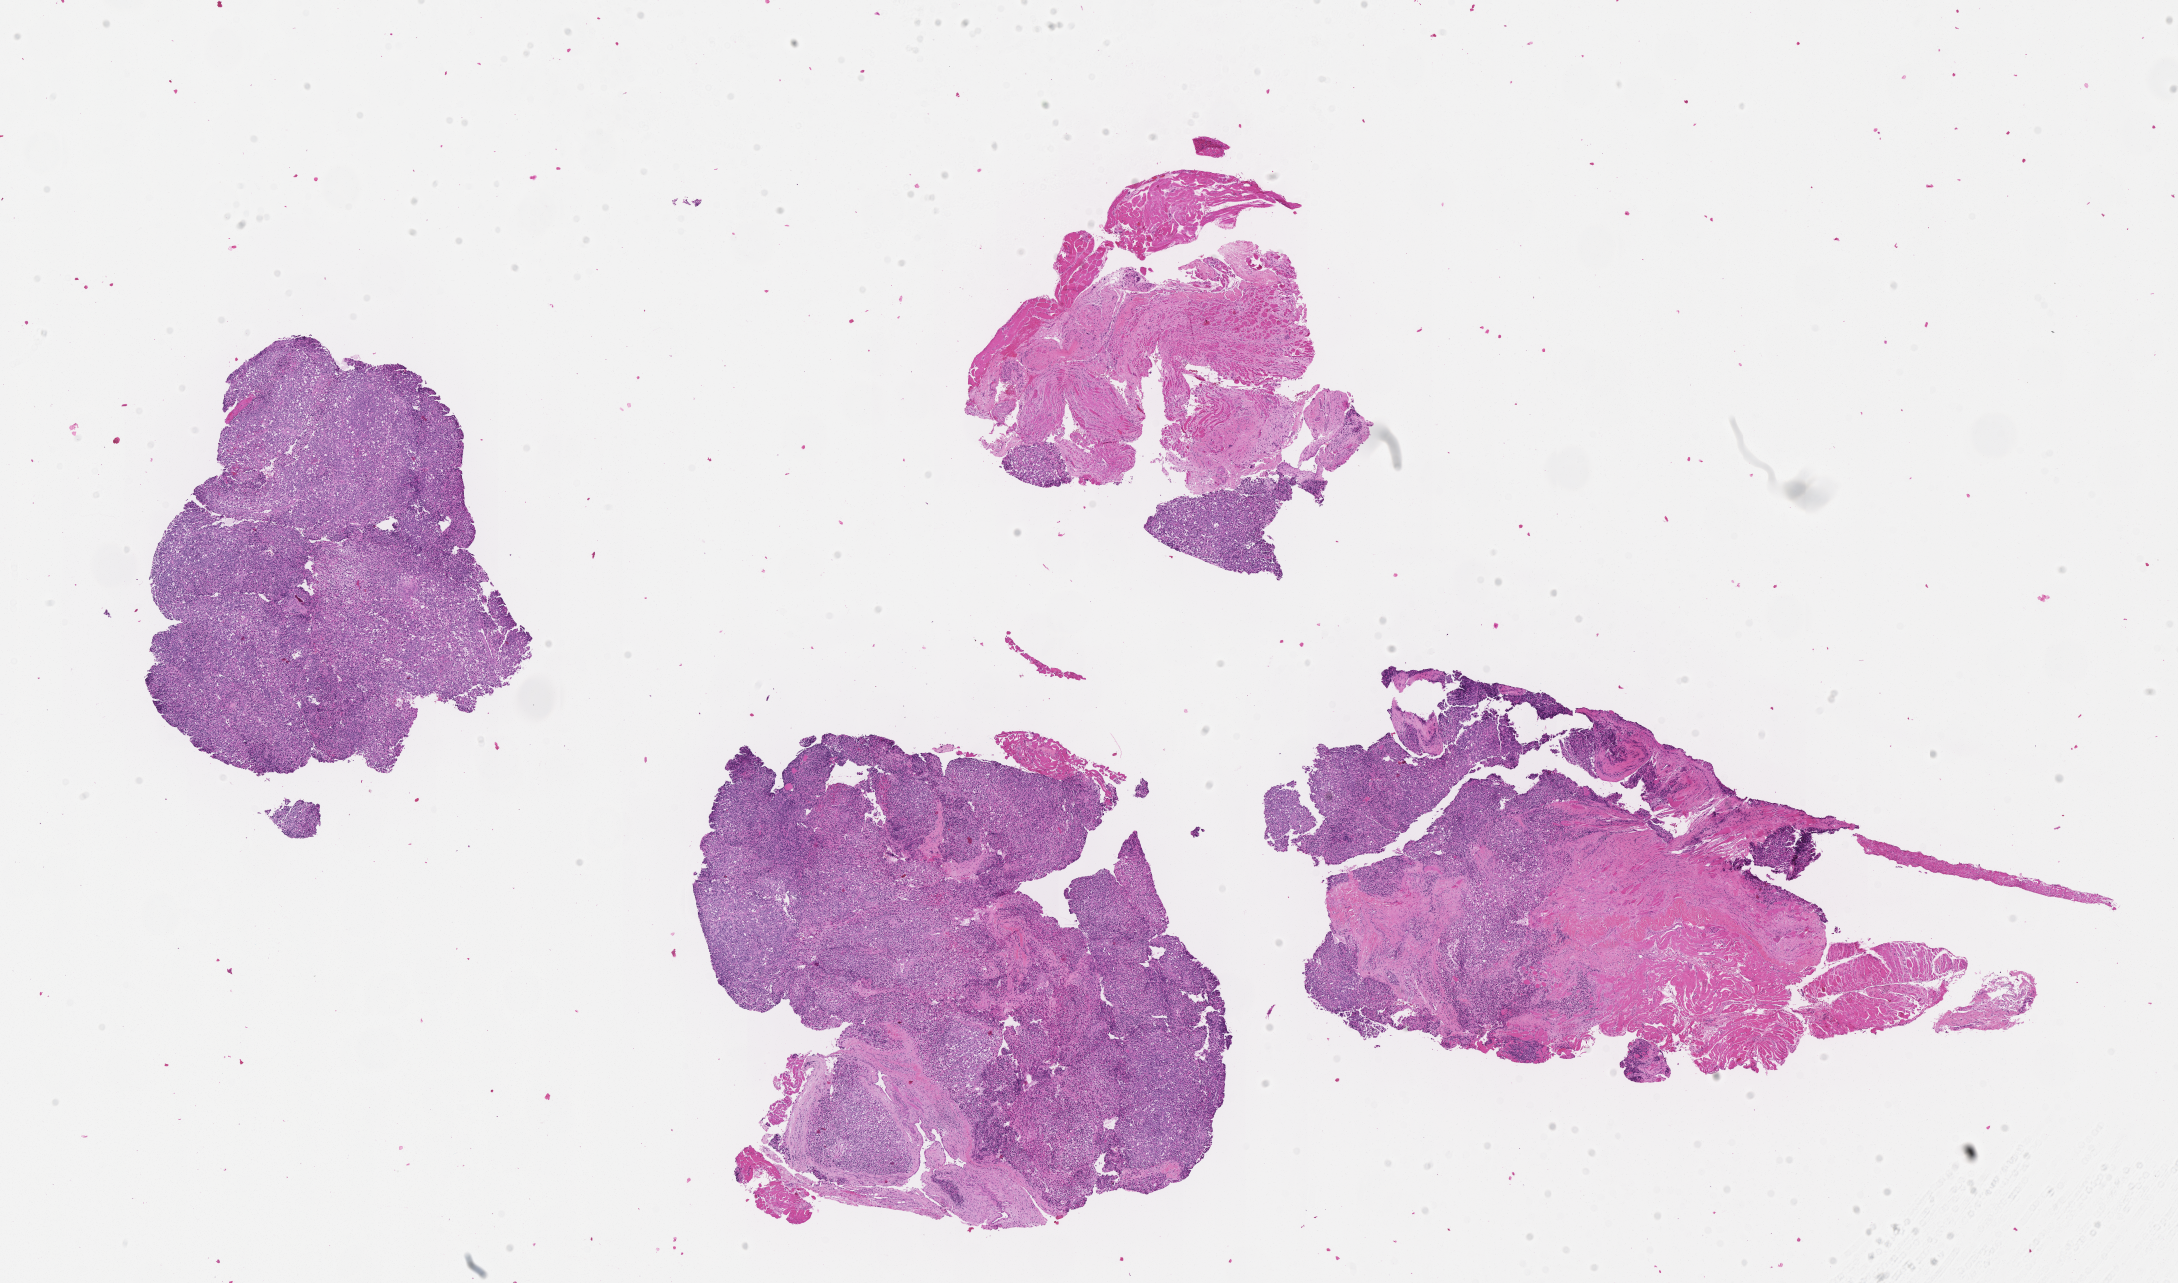
Digitized hematoxylin and eosin (H&E)-stained section of tumor tissue — a low-resolution overview of the entire scanned area, about 17.6 x 10.4 mm, FFPE section. Female patient, age at diagnosis 3.7 years.
Diagnosis: rhabdomyosarcoma; histological classification: embryonal rhabdomyosarcoma. Metastatic status at presentation (as recorded): non-metastatic. Stage (as recorded): 3.